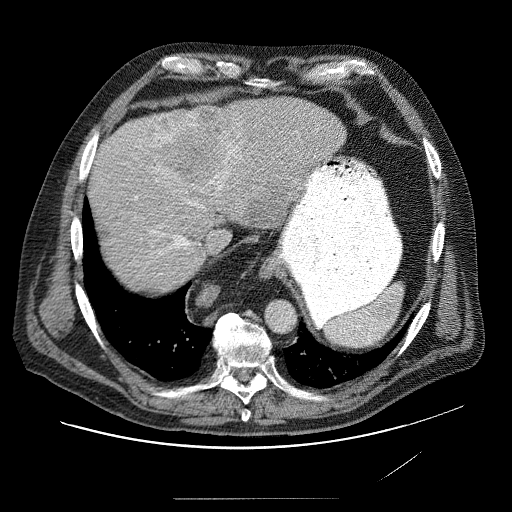
Contrast-enhanced abdominal CT (liver protocol), one axial slice; slice 66 of 89 in the series (ordered by position); 120 kVp; soft-tissue window (W 400 / L 40 HU); 512 × 512 image matrix, field of view 420 × 420 mm. From the clinical record (not read from this slice): diagnosis: hepatocellular carcinoma (patient treated with transarterial chemoembolisation; whether this scan precedes or follows treatment is not stated here); TNM stage (as recorded): Stage-IVA; Child-Pugh class: A; tumour differentiation: moderately differentiated; tumour nodularity: multinodular.
Outlined on this slice (semi-automatic segmentation, software-assisted and operator-edited):
- liver parenchyma outside the tumour (the mass and vessels are separate outlines, so this box may not span the whole liver): bounding box (x1, y1, x2, y2) in pixels: (88, 100, 344, 278)
- mass: (144, 108, 305, 224)
- liver vessels: (125, 134, 244, 249)